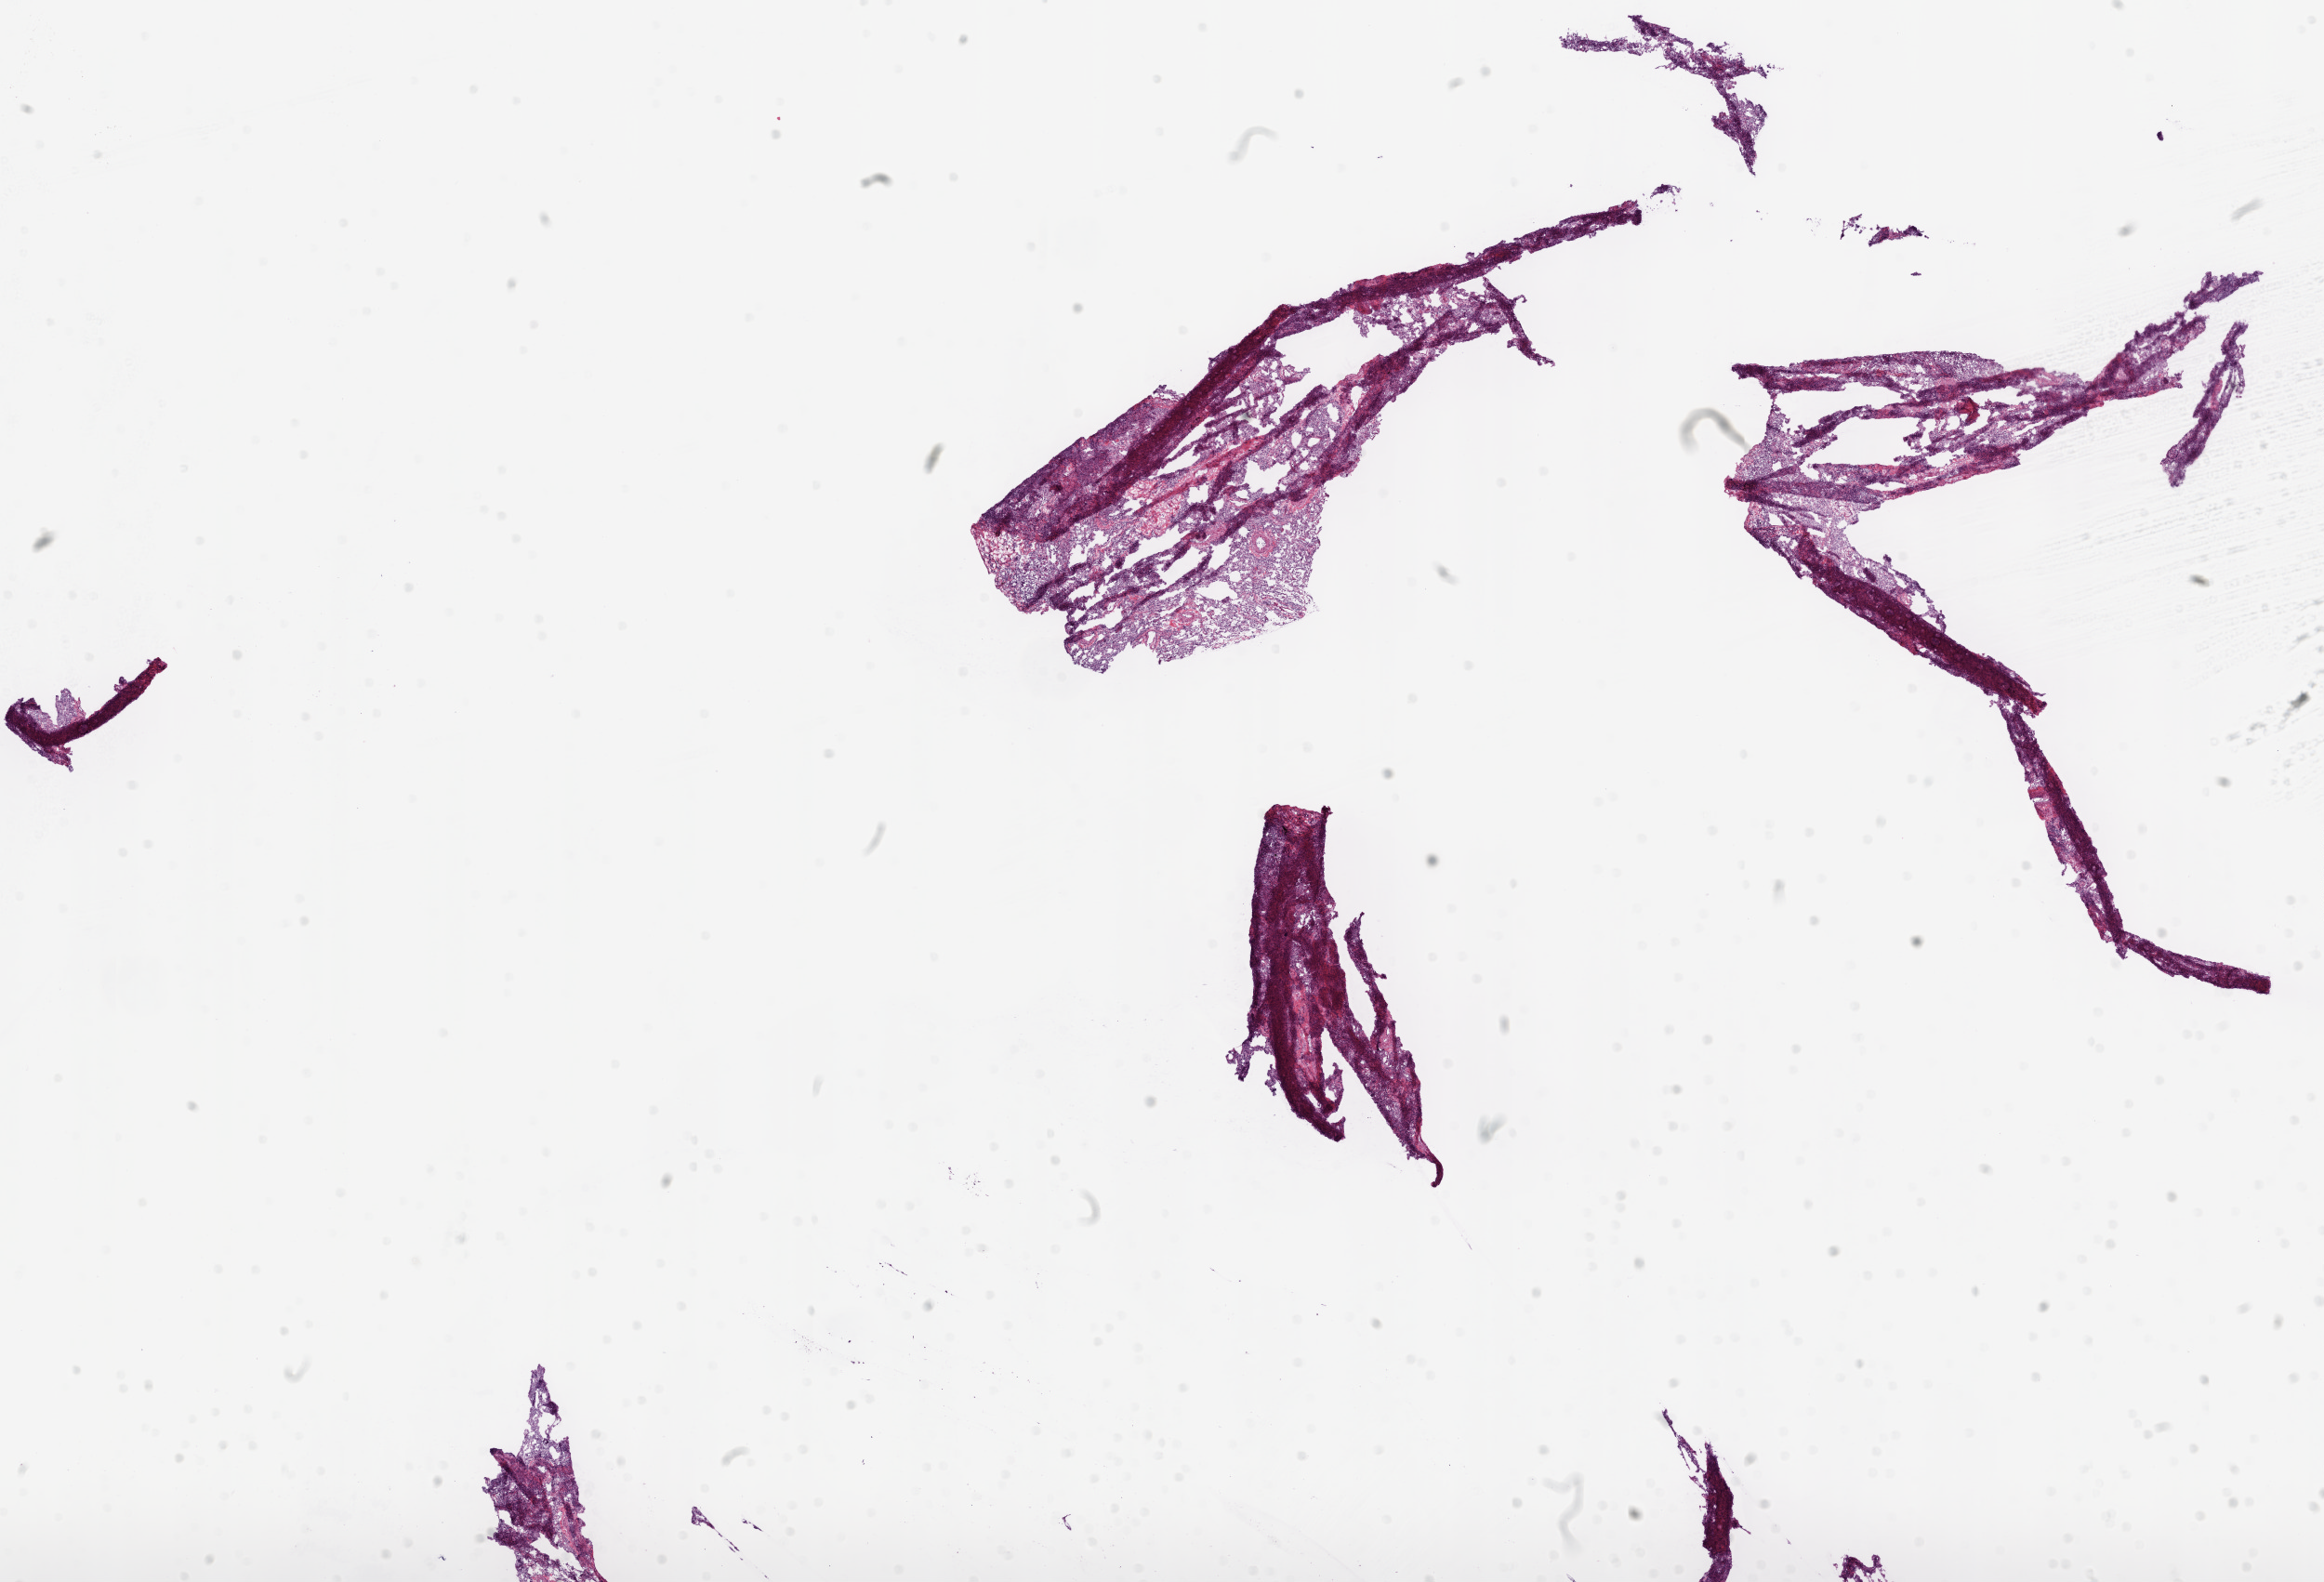
Whole-slide histology image, H&E-stained — shown as a low-resolution overview of the whole scanned area (about 20.1 x 13.7 mm), frozen section from the top of the tissue portion, lung, solid tissue normal (non-tumour tissue) sample. Male patient; age at initial diagnosis 68 years.
This section: solid tissue normal (non-tumour) sample from the same patient. Patient diagnosis: Squamous cell carcinoma, NOS (upper lobe, lung).